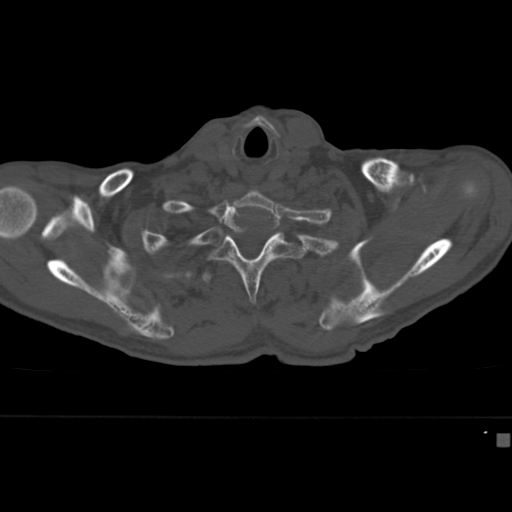
CT including the spine, one axial slice. Slice 346 of 430 in the series (ordered by position). 120 kVp. Bone window (W 1800 / L 400 HU). 1.5 mm slice thickness. 512 × 512 image matrix, field of view 337 × 337 mm. Patient: male, 64 years. Case-level facts recorded for this patient, not image findings: primary cancer: uterus; vertebrae with lytic lesions (as recorded): T1, T4, T5, T7, L5.
Outlined on this slice (semi-automatically segmented with operator editing):
- T2 vertebra: bounding box [x1, y1, x2, y2] px = [206, 233, 306, 304]
- T3 vertebra: [202, 260, 276, 284]